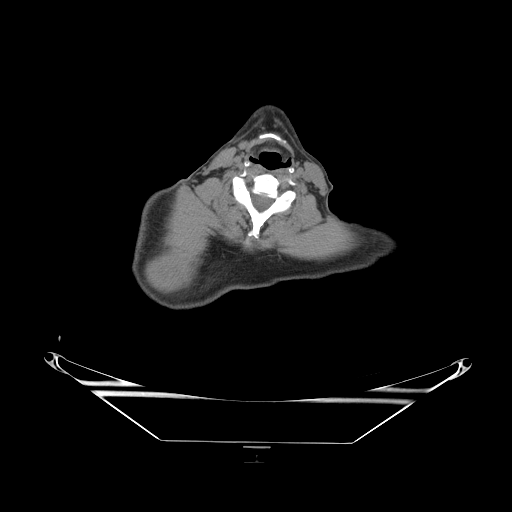
CT of an extremity soft-tissue mass (from a PET/CT study), one axial slice. Slice 221 of 267 in the series (ordered by position). Soft-tissue window (W 400 / L 40 HU). 512 × 512 image matrix, field of view 500 × 500 mm. Male patient. Case-level facts recorded for this patient, not image findings: histological type: pleiomorphic spindle cell undifferentiated; grade: high; site of the primary tumour: right parascapusular.
Structures marked on this image (expert contour drawn on MRI and transferred to this co-registered scan by the dataset authors):
- gross tumour volume including surrounding oedema: bounding box [x1, y1, x2, y2] px = [149, 267, 197, 293]
- gross tumour volume (mass): [151, 267, 170, 289]